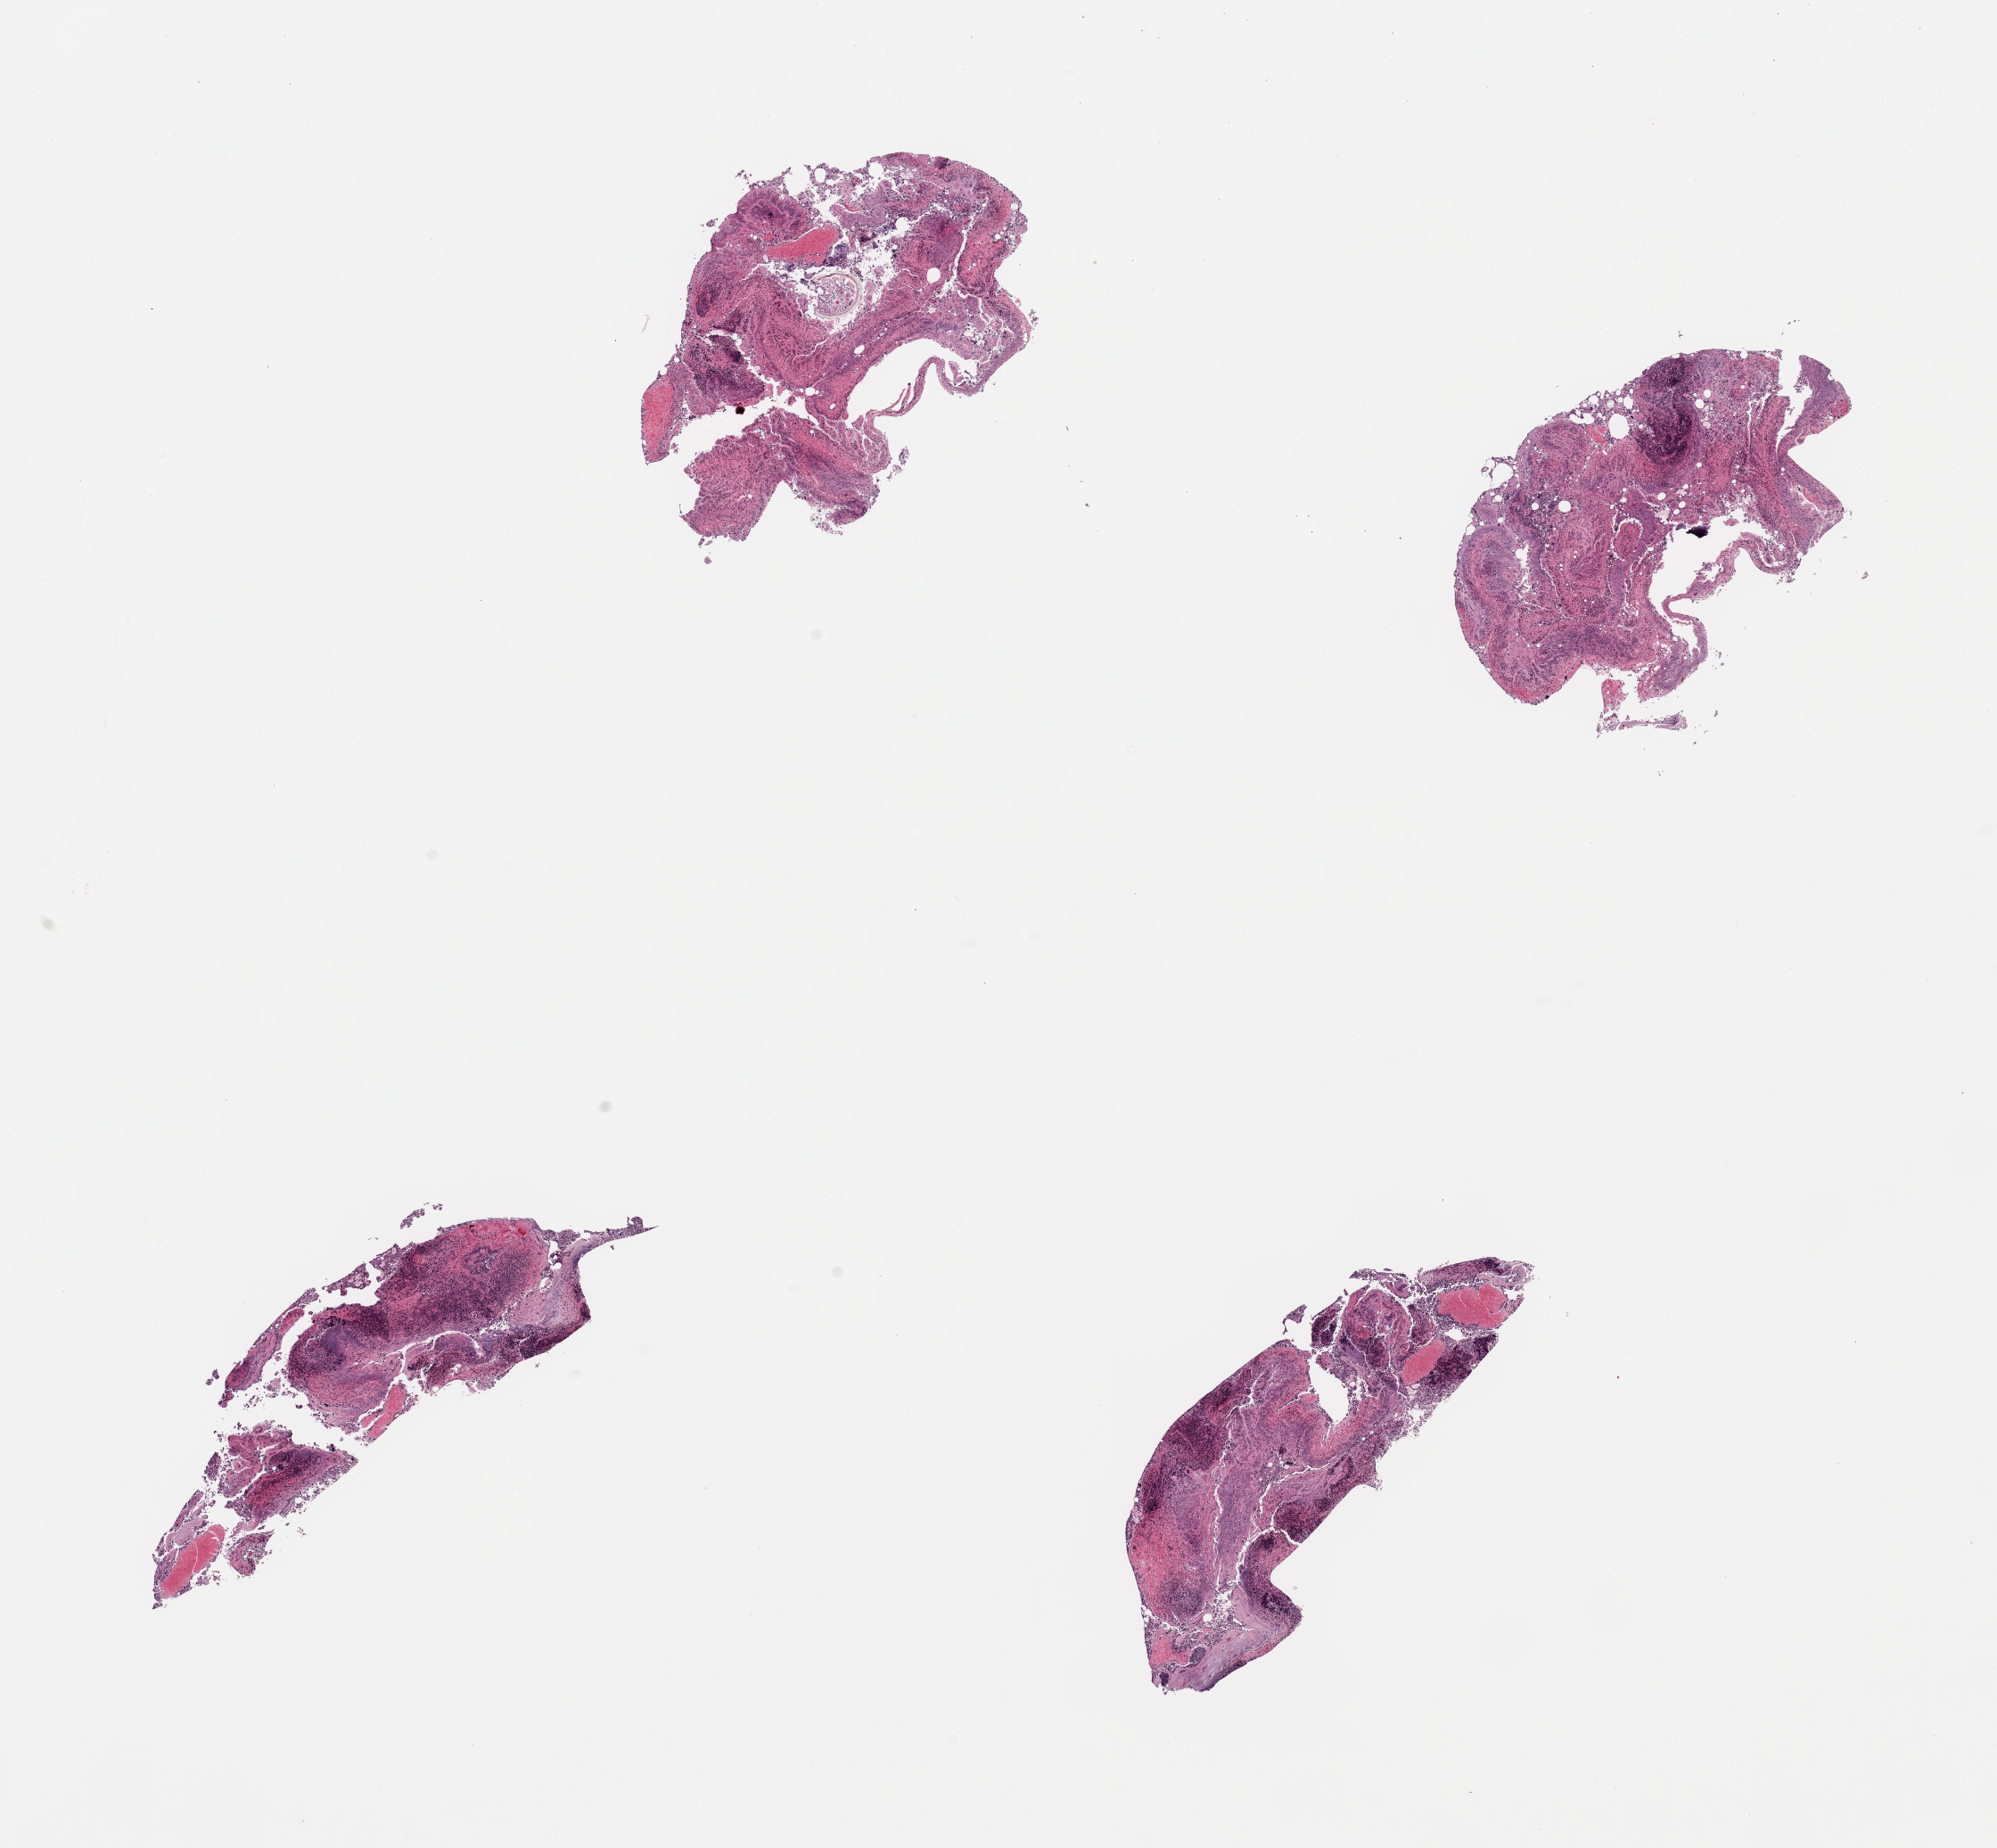
Haematoxylin and eosin whole-slide image, a low-resolution overview of the entire scanned area, about 17.7 x 16.4 mm (acquisition: 20x scan), PAXgene-fixed paraffin-embedded (PFPE) section, target tissue: ileum, tissue donor sample. Male donor.
- pathologist's review note for this sample: 4 pieces, mucosa autolyzed but residual target lymphoid aggregates are ~20% of tissue